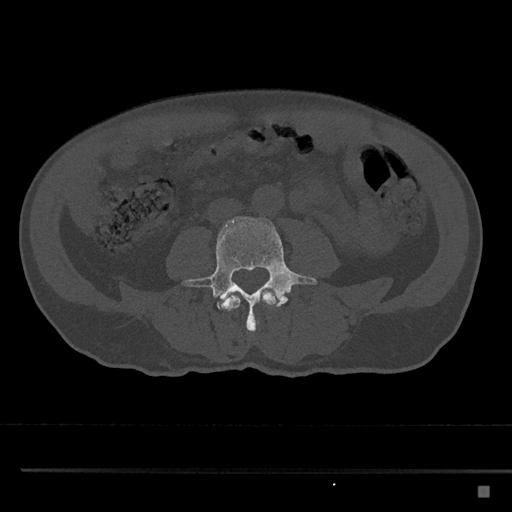
CT including the spine, one axial slice; slice 650 of 797 in the series (ordered by position); reconstruction kernel Br40s/3; 120 kVp; bone window (W 1800 / L 400 HU); 0.5 mm slice thickness; 512 × 512 image matrix, field of view 391 × 391 mm. Patient: male, 59 years. Case-level facts recorded for this patient, not image findings: primary cancer: prostate.
Annotated regions visible in this slice (semi-automatically segmented with operator editing):
- L3 vertebra: bounding box <222,291,277,320> (left, top, right, bottom; pixels)
- L4 vertebra: <182,217,318,335>